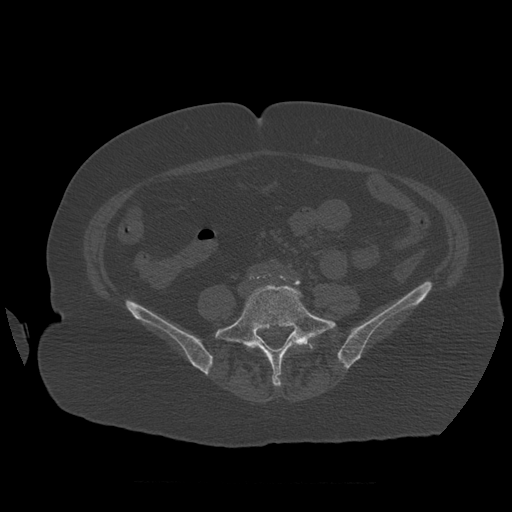
CT including the spine, one axial slice. Slice 186 of 399 in the series (ordered by position). Reconstruction kernel STANDARD. 120 kVp. Bone window (W 1800 / L 400 HU). 1.25 mm slice thickness. 512 × 512 image matrix. Patient age 81 years. From the clinical record (not read from this slice): primary cancer: renal.
Outlined on this slice (semi-automatically segmented with operator editing):
- L4 vertebra: bounding box <253,345,273,368> (left, top, right, bottom; pixels)
- L5 vertebra: <215,284,336,387>